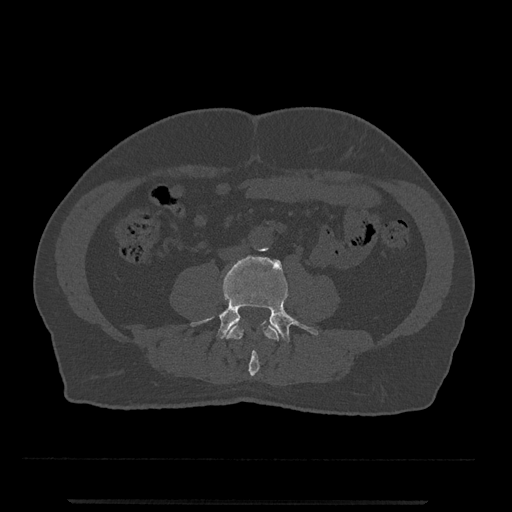
CT including the spine, one axial slice; slice 158 of 797 in the series (ordered by position); reconstruction kernel Br40s/3; 120 kVp; bone window (W 1800 / L 400 HU); 0.5 mm slice thickness; 512 × 512 image matrix. Male patient, age 63 years. Case-level facts recorded for this patient, not image findings: primary cancer: prostate.
Outlined on this slice (semi-automatically segmented with operator editing):
- L3 vertebra: bounding box [x1, y1, x2, y2] px = [226, 323, 281, 377]
- L4 vertebra: [190, 255, 319, 342]